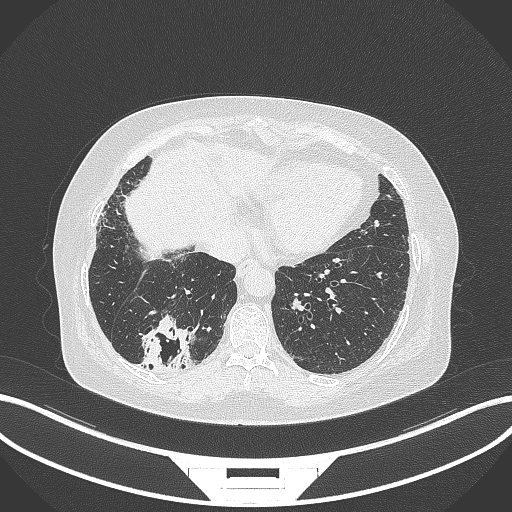
Chest CT, one axial slice; slice 55 of 296 in the series (ordered by position); lung window (W 1500 / L -600 HU); 512 × 512 image matrix. Patient: female, 65 years. From the clinical record (not read from this slice): clinical TNM (as recorded): T2b N1 M0.
Outlined on this slice (rectangle marked by the reading radiologist):
- lung tumour (recorded histology: adenocarcinoma): box from (x=133, y=313) to (x=199, y=373) px